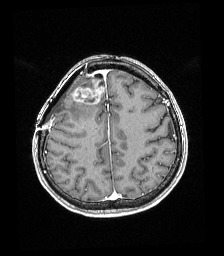
Brain MRI from a brain-tumour surgery series, one axial slice; position 61 of 192 along the scan axis; T1-weighted post-contrast; 1 mm slice thickness; 224 × 256 image matrix, field of view 219 × 250 mm. Case-level facts recorded for this patient, not image findings: histopathology: Astrocytoma; WHO grade: 4; IDH mutation: yes; tumour location: Right superficial frontal.
Structures marked on this image (manually delineated by an expert):
- tumour: bounding box (x1, y1, x2, y2) in pixels: (71, 80, 105, 105)